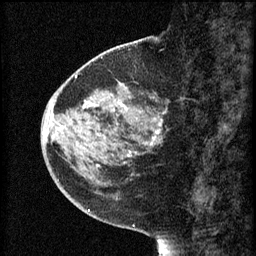
Breast MRI (dynamic contrast-enhanced), one sagittal slice. Slice 24 of 60 in the series (ordered by position). 3 images stored at this slice position (order not interpretable as contrast timing). 1.5 T. TE 4.2 ms, TR 8.2 ms. 2 mm slice thickness. 256 × 256 image matrix, field of view 180 × 180 mm. Patient: female, 44 years.
Annotated regions visible in this slice (semi-automatically segmented with operator editing):
- analysis volume of interest (the breast-tissue region the enhancement analysis was run in; not a lesion): bounding box [x1, y1, x2, y2] px = [73, 82, 169, 165]
- tumour enhancement mask (voxels above the 70 % enhancement threshold inside the analysis volume of interest): [87, 102, 165, 157]